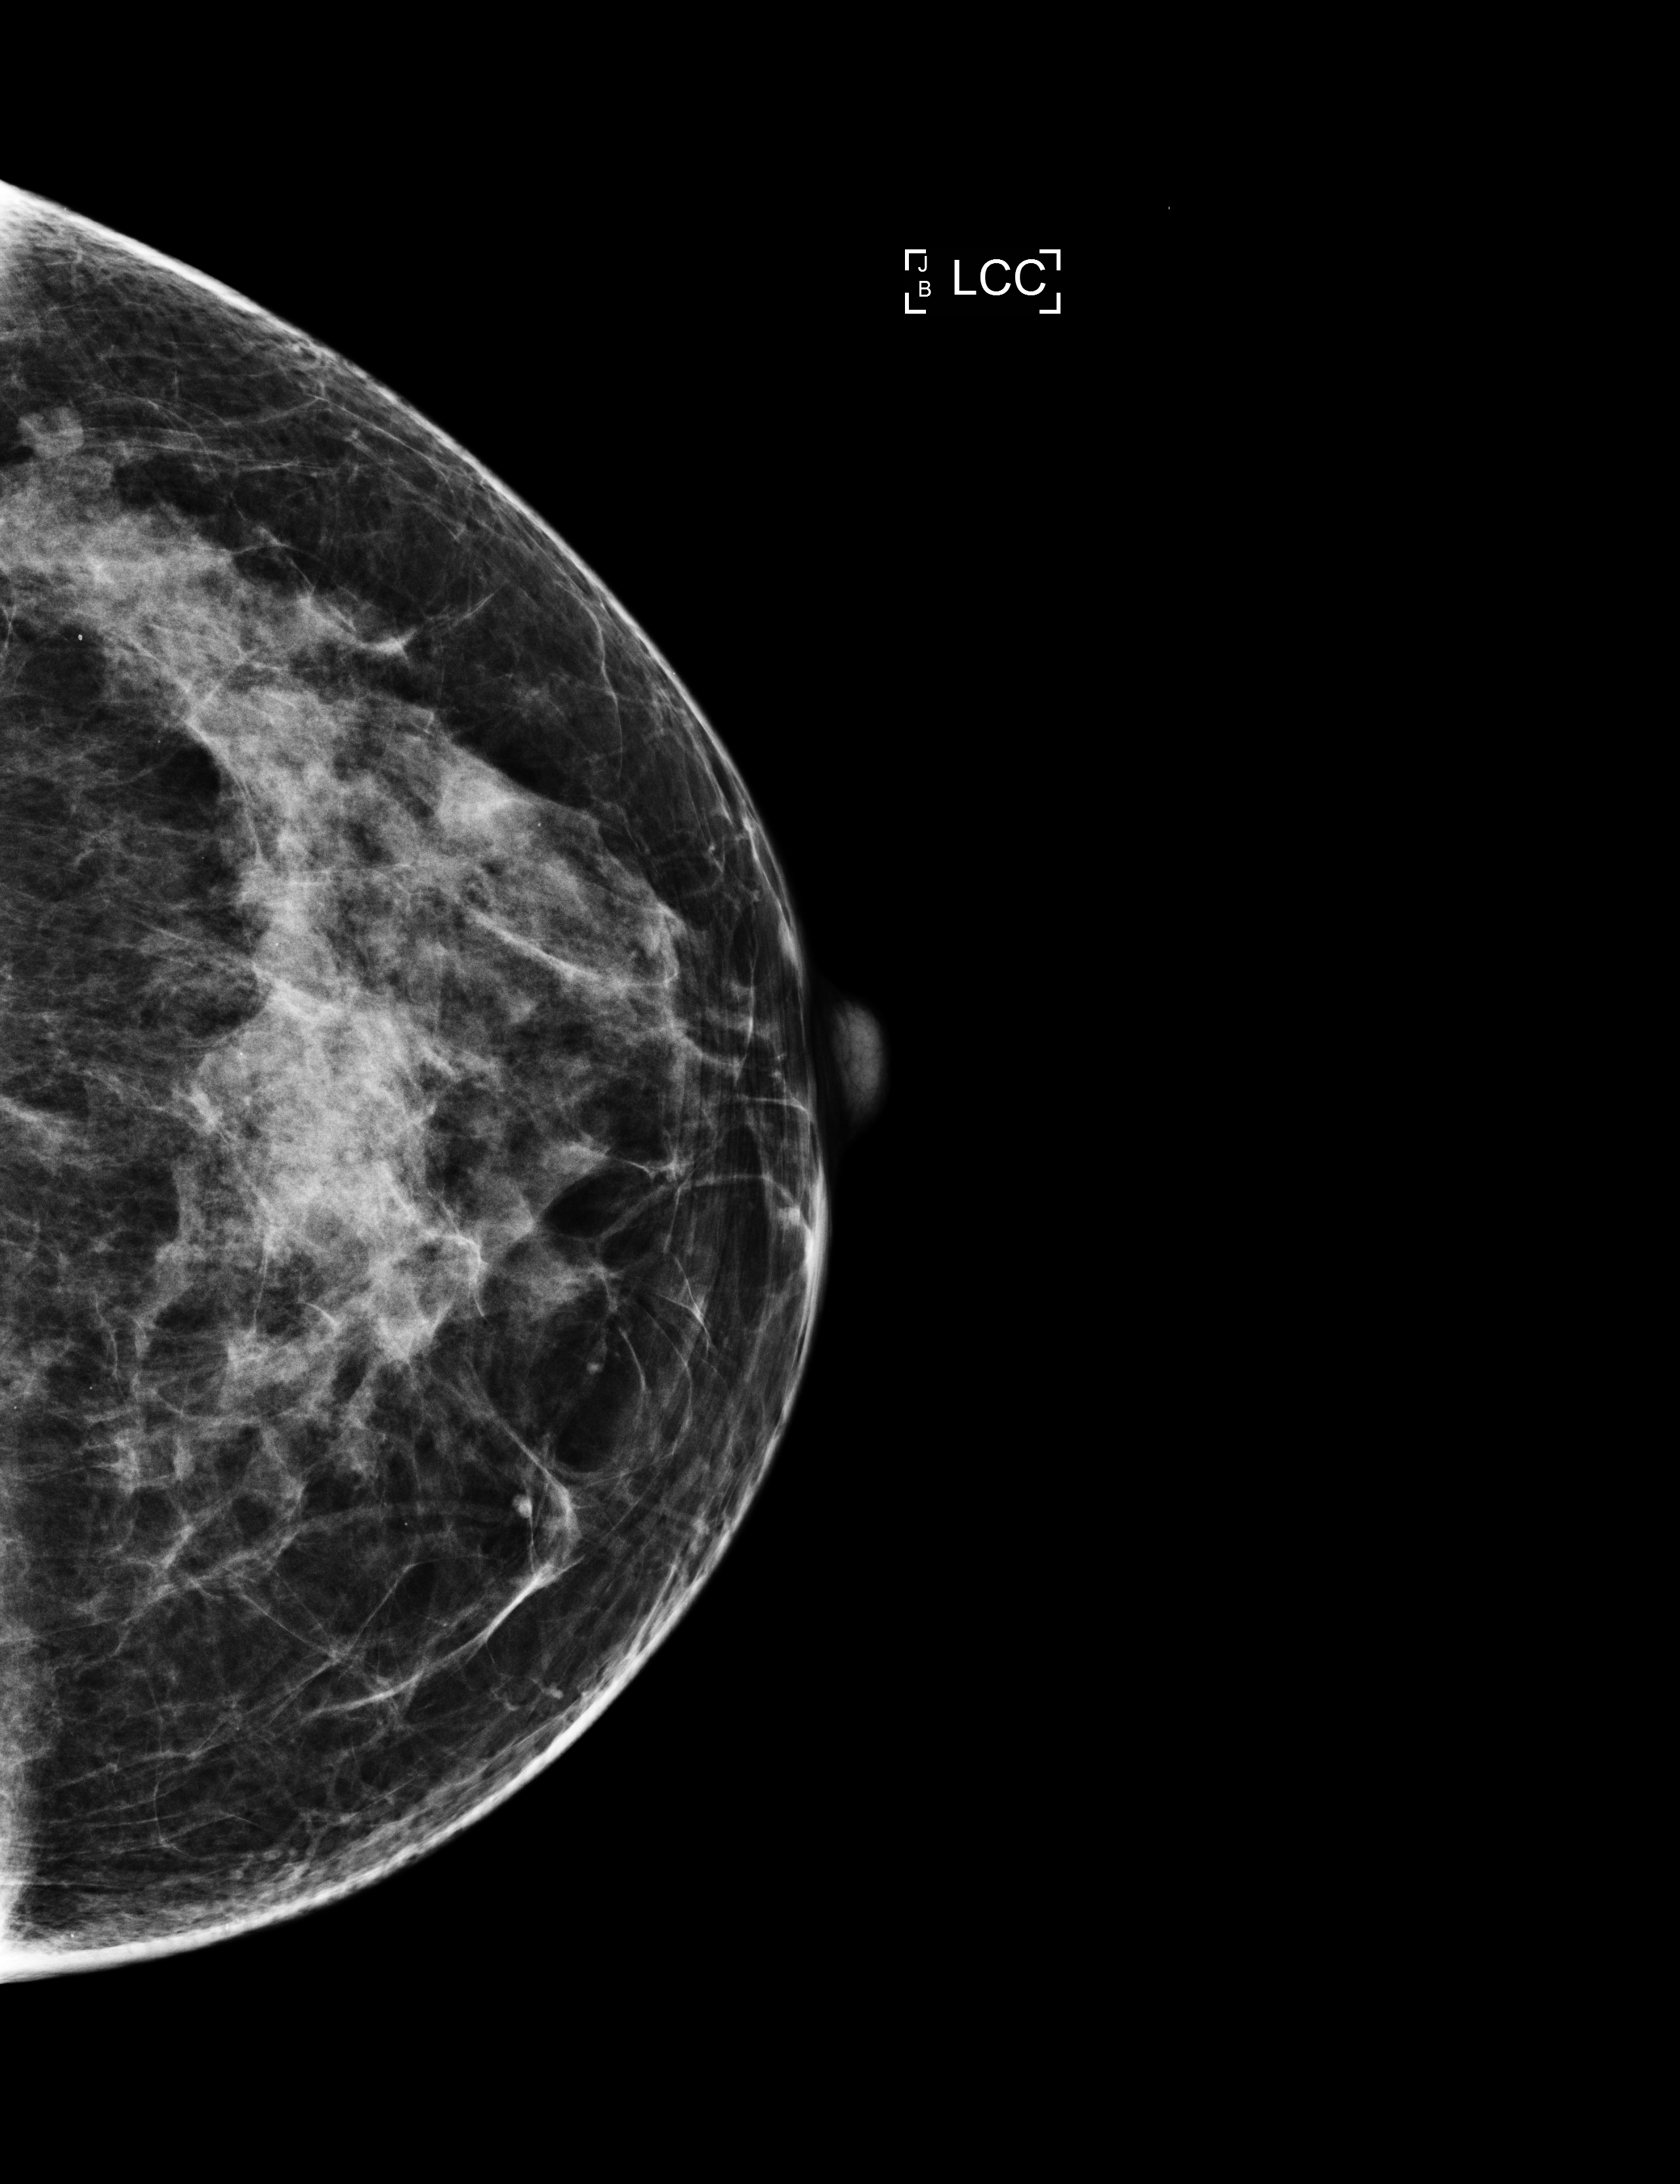
Annual screening mammography examination. Patient: female, 61 years.
Image type: full-field digital mammogram. Breast: left. Projection: CC view.